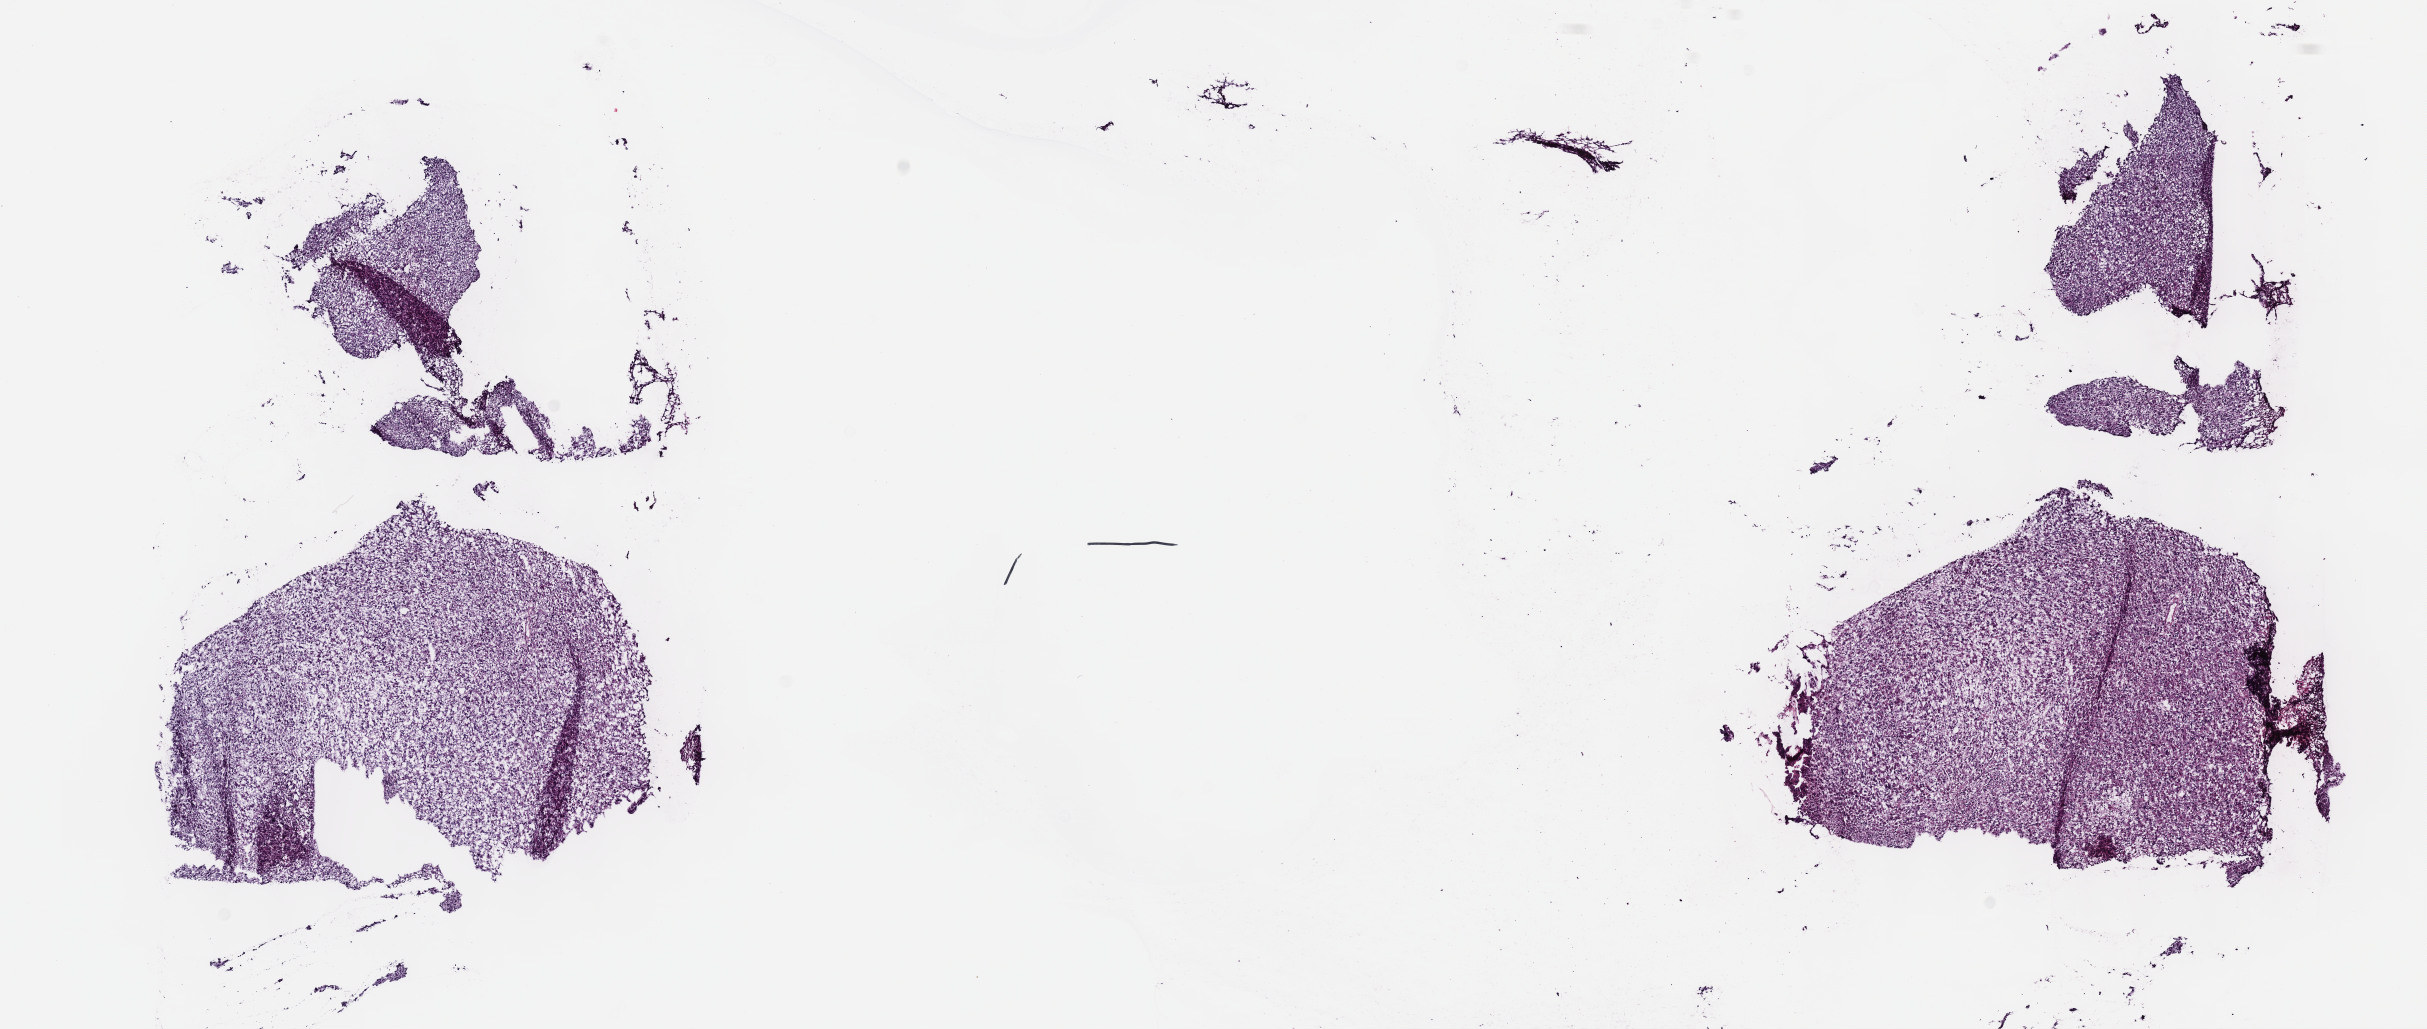
H&E-stained whole-slide image — shown as a low-resolution overview of the whole scanned area (about 19.6 x 8.3 mm), frozen section from the top of the tissue portion, primary tumour sample from the brain. Patient: male, age at initial diagnosis 57 years. Histologic grade: G3 (poorly differentiated). Slide review estimates, as recorded: tumour cells 50%, tumour nuclei 90%, normal cells 5%, stromal cells 45%, necrosis 0%. Infiltration values recorded for this section: lymphocyte infiltration 0%, monocyte infiltration 0%, neutrophil infiltration 0%.
Laterality: left. Pathologic diagnosis: Astrocytoma, anaplastic (cerebrum).